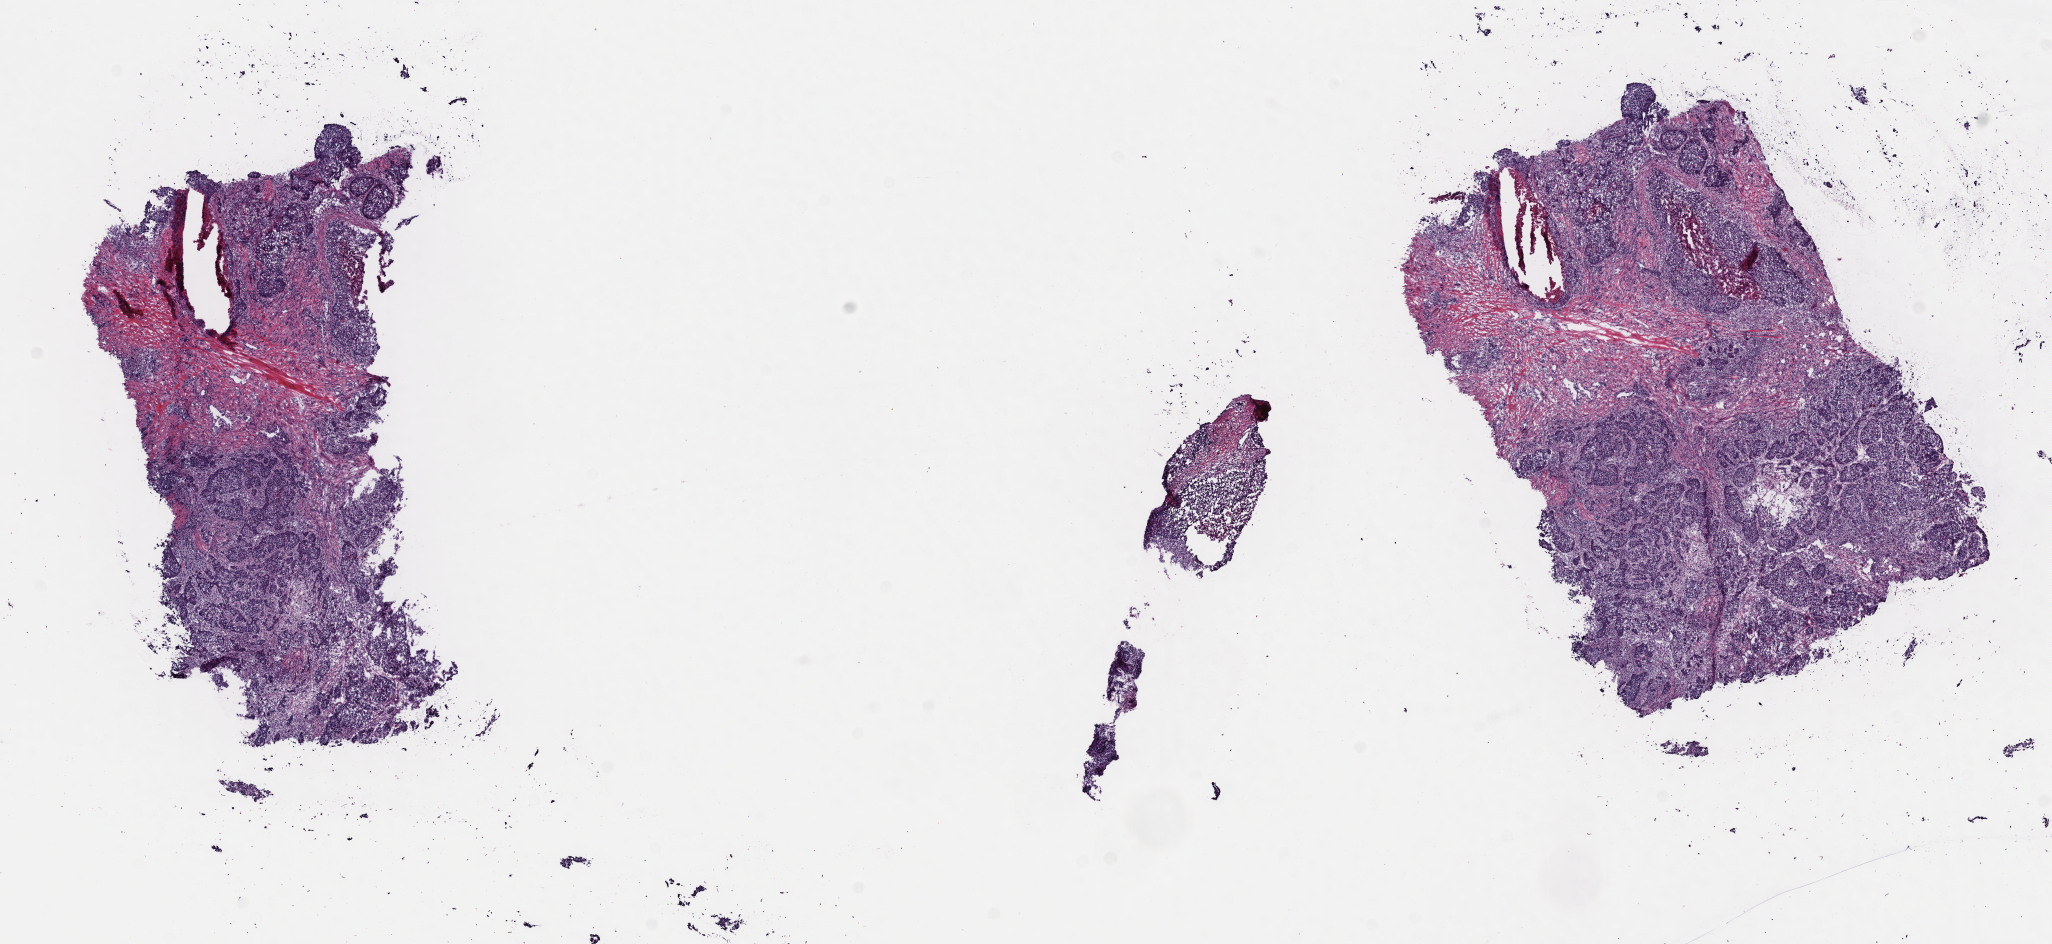
Hematoxylin and eosin (H&E) stained whole-slide image — a low-resolution overview of the entire scanned area, about 16.2 x 7.4 mm (from a 40x scan). Frozen section. Sample: primary tumour, breast. Female, age 69 years at initial diagnosis. Pathologist review of this section (percent, as recorded): tumour cells 70%, tumour nuclei 90%, normal cells 0%, stromal cells 23%, necrosis 7%. Infiltration values recorded for this section: lymphocyte infiltration 3%, monocyte infiltration 0%, neutrophil infiltration 0%.
- AJCC pathologic stage: IIA (7th edition)
- pathologic diagnosis: Infiltrating duct carcinoma, NOS
- laterality: right
- TNM: T2 N0 M0